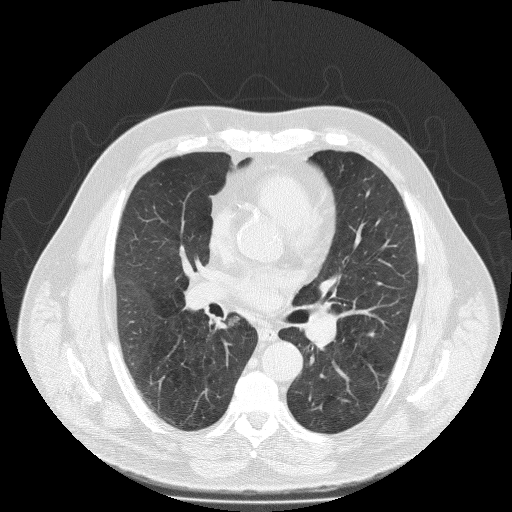
Axial slice from a low-dose chest CT screening exam. First (baseline) screen. Lung window (W 1500 / L -600 HU). Lung (sharp) reconstruction kernel (FC51). 120 kVp. Slice 98 of 204 in the series. 512 × 512 image matrix, field of view 430 × 430 mm. Male participant, aged 65 years at enrolment. Former smoker at enrolment.
- Expert reader's lesion annotation, box from (x=214, y=308) to (x=247, y=335) px.
- The screening reader recorded 2 non-calcified nodules or masses ≥4 mm on this exam; which of them this box marks is not recorded.
- Participant outcome: lung cancer diagnosed 651 days after this screen (after the second annual screen) — large cell neuroendocrine carcinoma, right lower lobe, undifferentiated (G4), stage IIIA (AJCC 6th edition).